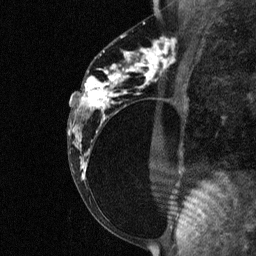
Breast MRI (dynamic contrast-enhanced), one sagittal slice. Slice 34 of 64 in the series (ordered by position). Dynamic contrast-enhanced study with each time point stored as its own series, time point 2 of 3 at this slice position (early post-contrast, ordered by acquisition time). 1.5 T. TE 4.8 ms, TR 27 ms. 2 mm slice thickness. 256 × 256 image matrix. Female patient, age 34 years. From the clinical record (not read from this slice): setting: breast cancer imaged before/during neoadjuvant chemotherapy; receptor status: HR-positive, HER2-negative.
Outlined on this slice (semi-automatically segmented with operator editing):
- analysis volume of interest (the breast-tissue region the enhancement analysis was run in; not a lesion): box from (x=78, y=44) to (x=181, y=191) px
- tumour enhancement mask (voxels above the 90 % enhancement threshold inside the analysis volume of interest): (x=82, y=44)–(x=168, y=167)